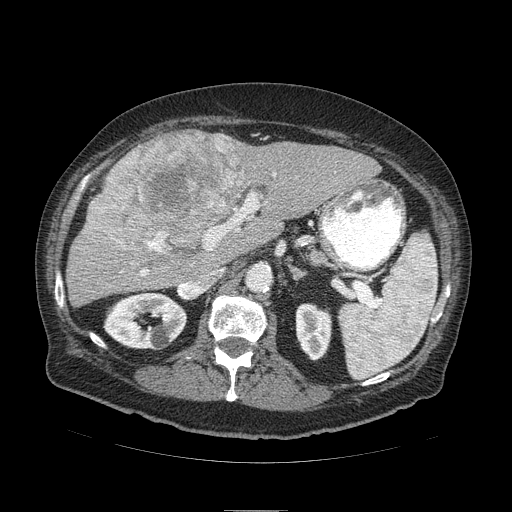
Contrast-enhanced abdominal CT (liver protocol), one axial slice; position 51 of 103 along the scan axis; reconstruction kernel STANDARD; 120 kVp; soft-tissue window (W 400 / L 40 HU); 512 × 512 image matrix. Case-level facts recorded for this patient, not image findings: diagnosis: hepatocellular carcinoma (patient treated with transarterial chemoembolisation; whether this scan precedes or follows treatment is not stated here); TNM stage (as recorded): Stage-IIIA.
Structures marked on this image (semi-automatically segmented with operator editing):
- liver parenchyma outside the tumour (the mass and vessels are separate outlines, so this box may not span the whole liver): bounding box (x1, y1, x2, y2) in pixels: (66, 134, 380, 306)
- mass: (84, 129, 250, 258)
- liver vessels: (140, 173, 276, 276)